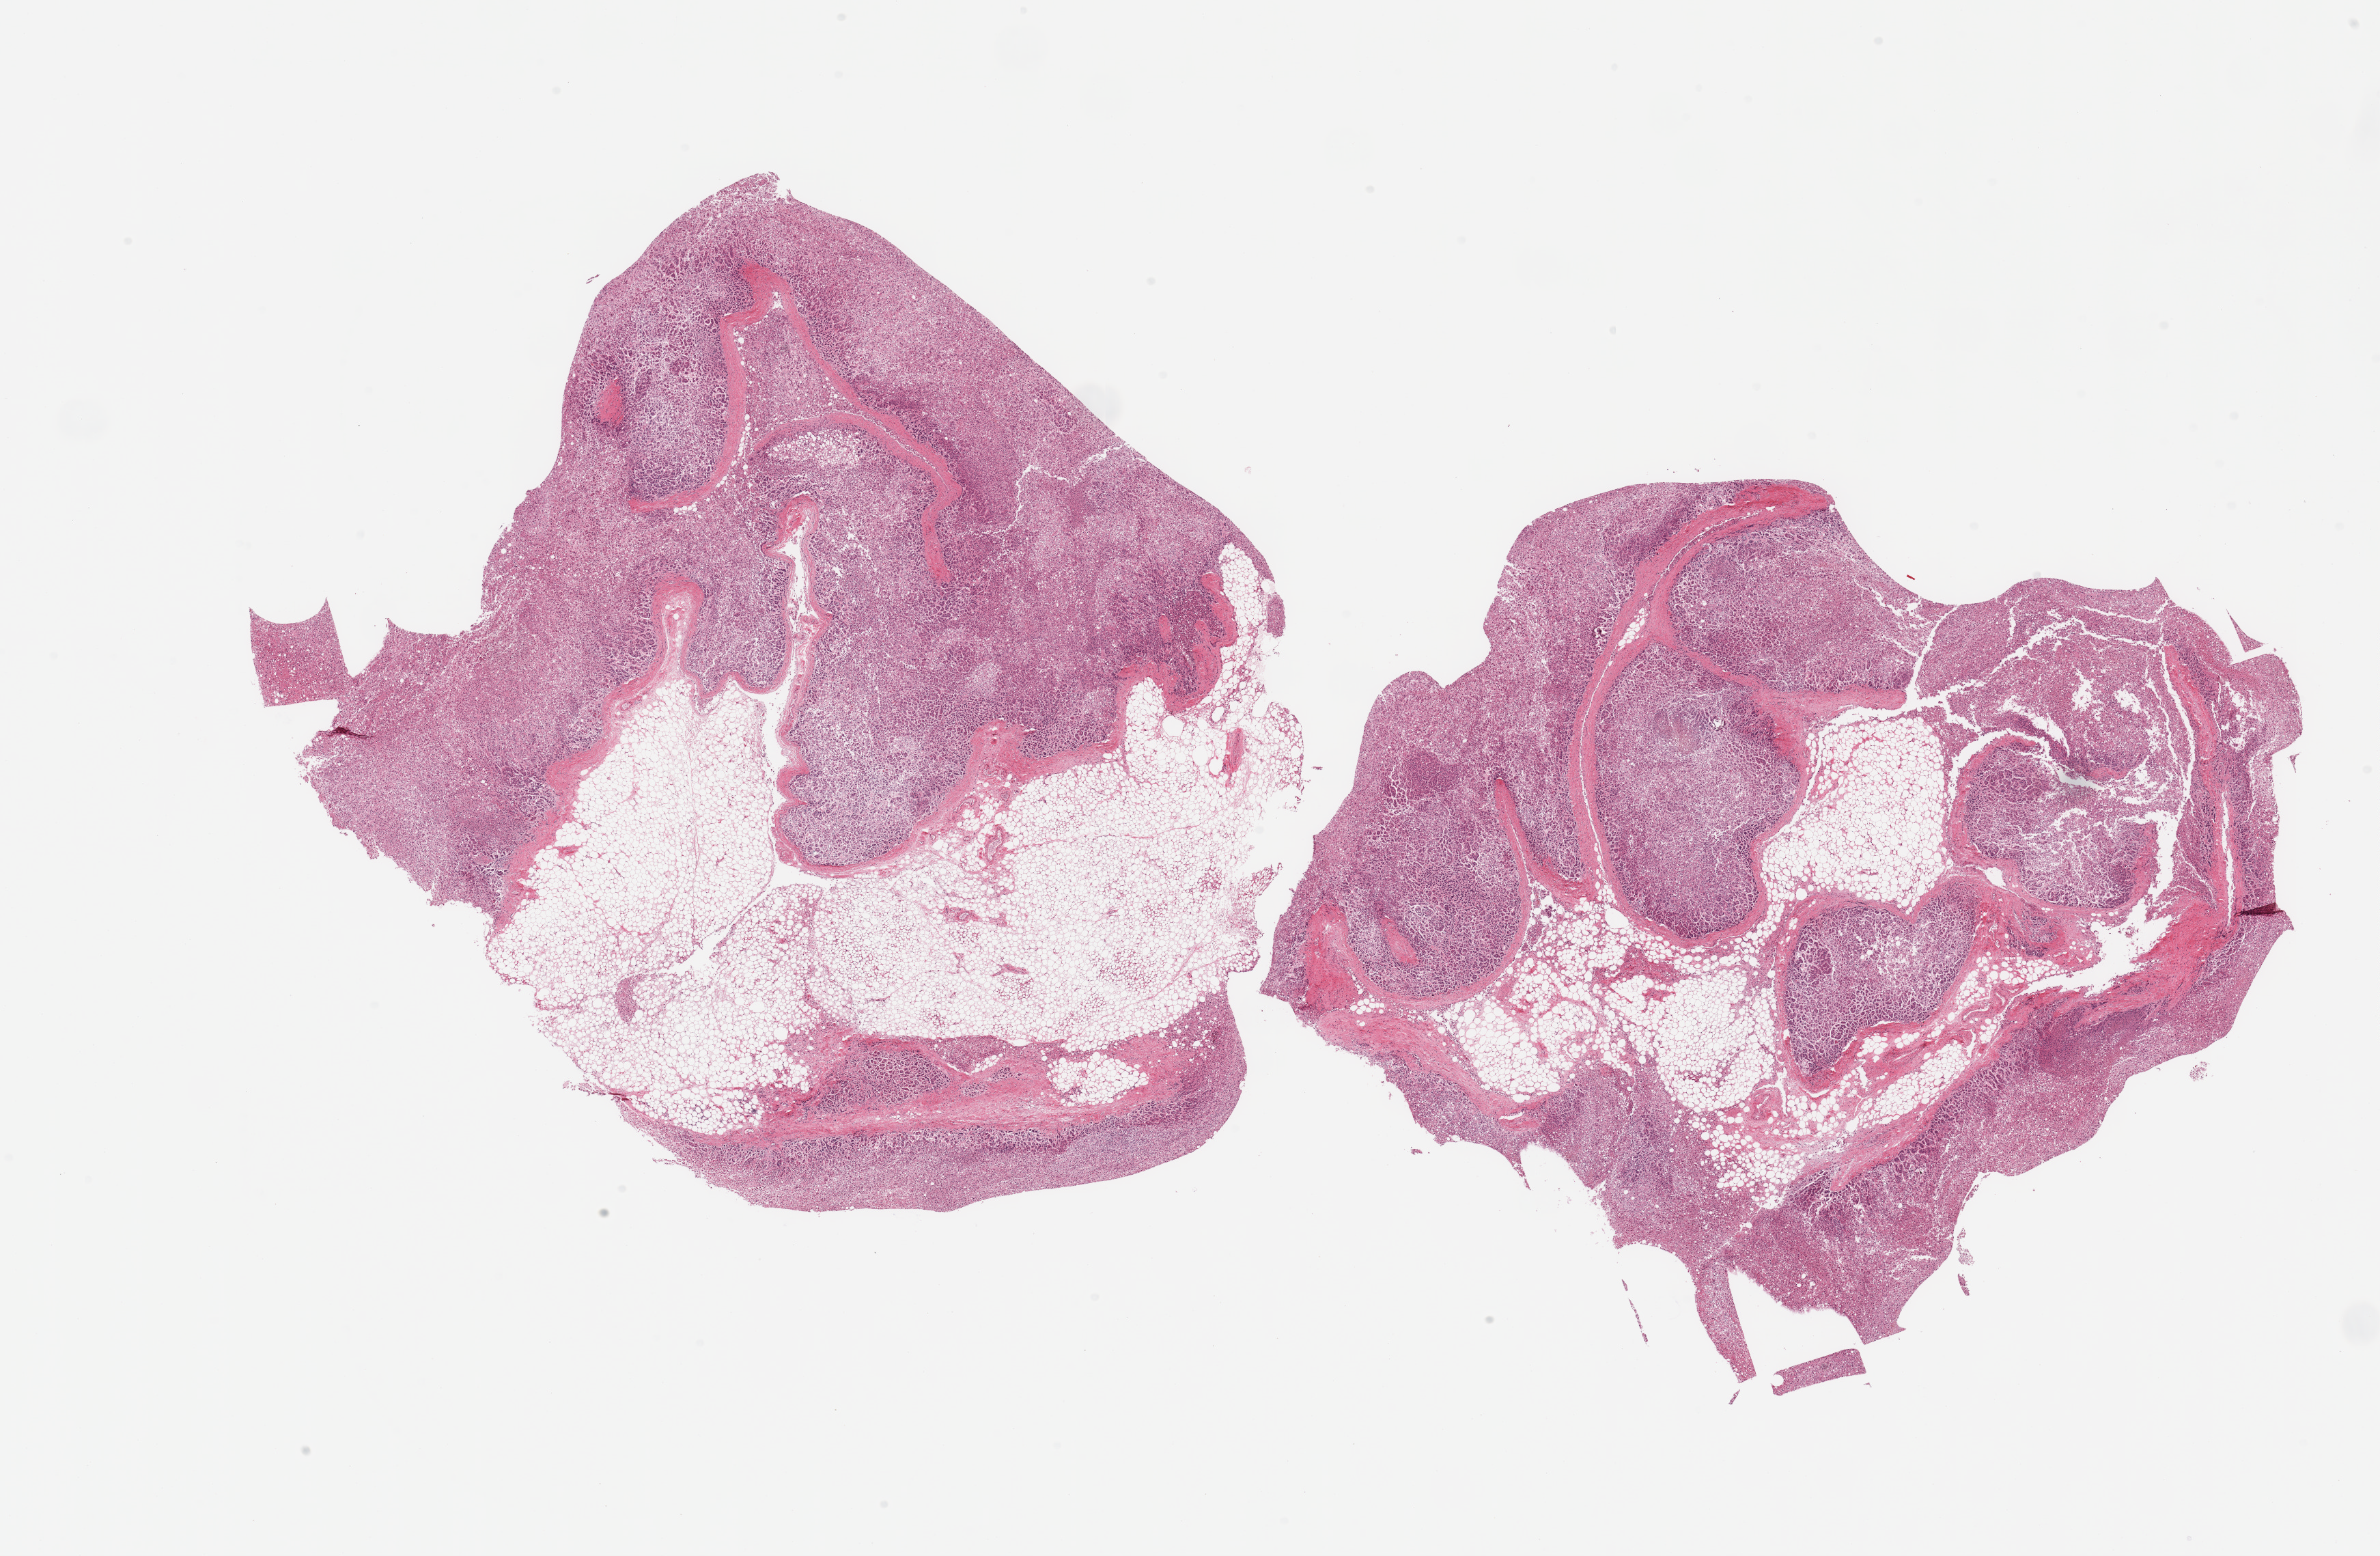
H&E whole-slide image, whole scanned area (about 27.6 x 18.0 mm) shown as a low-resolution overview. PAXgene-fixed paraffin-embedded (PFPE) section. Target tissue: adrenal gland. Tissue donor sample. Donor sex: male.
Review note (as recorded): 2 pieces; mildly to moderately autolyzed adrenal cortex; 40% and 30% internal fat.